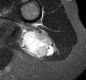
MRI of an extremity soft-tissue mass, one axial slice; slice 12 of 30 in the series (ordered by position); STIR; MR volume resampled by the dataset authors to the PET/CT grid (not the native acquisition matrix); 3.27 mm slice thickness; 86 × 80 image matrix. Female patient. Case-level facts recorded for this patient, not image findings: histological type: malignant fibrous histiocytoma; grade: low; site of the primary tumour: left arm.
Structures marked on this image (expert contour drawn on MRI and transferred to this co-registered scan by the dataset authors):
- gross tumour volume (mass): bounding box <17,24,55,59> (left, top, right, bottom; pixels)